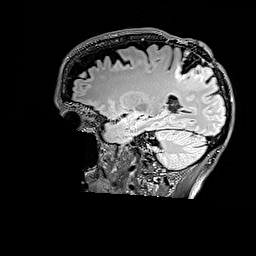
Brain MRI from a brain-tumour surgery series, one sagittal slice; slice 115 of 176 in the series (ordered by position); T2 FLAIR; 256 × 256 image matrix. Case-level facts recorded for this patient, not image findings: histopathology: Astrocytoma; WHO grade: 3; IDH mutation: yes; tumour location: Right Parietal.
Structures marked on this image (expert manual segmentation):
- tumour: bounding box (x1, y1, x2, y2) in pixels: (175, 60, 213, 82)
- tumour: (191, 62, 213, 81)